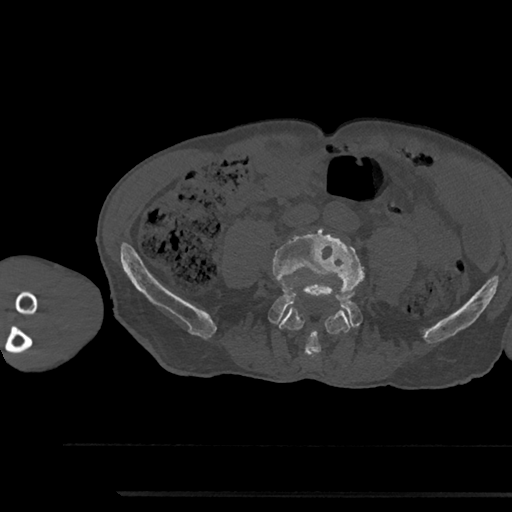
CT including the spine, one axial slice; position 385 of 797 along the scan axis; reconstruction kernel Br40s/3; bone window (W 1800 / L 400 HU); 0.5 mm slice thickness; 512 × 512 image matrix, field of view 367 × 367 mm. Male patient, age 79 years. From the clinical record (not read from this slice): primary cancer: prostate.
Structures marked on this image (semi-automatically segmented with operator editing):
- L4 vertebra: bounding box [x1, y1, x2, y2] px = [272, 229, 363, 357]
- L5 vertebra: [270, 295, 361, 327]